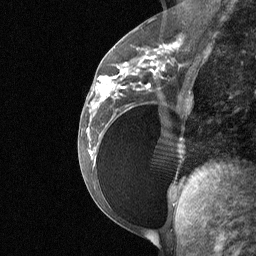
Breast MRI (dynamic contrast-enhanced), one sagittal slice; position 28 of 64 along the scan axis; dynamic contrast-enhanced study with each time point stored as its own series, time point 2 of 3 at this slice position (early post-contrast, ordered by acquisition time); 1.5 T; TE 4.8 ms, TR 27 ms; 256 × 256 image matrix, field of view 200 × 200 mm. Female patient, age 34 years. From the clinical record (not read from this slice): setting: breast cancer imaged before/during neoadjuvant chemotherapy; receptor status: HR-positive, HER2-negative.
Annotated regions visible in this slice (semi-automatically segmented with operator editing):
- analysis volume of interest (the breast-tissue region the enhancement analysis was run in; not a lesion): box from (x=92, y=50) to (x=188, y=185) px
- tumour enhancement mask (voxels above the 90 % enhancement threshold inside the analysis volume of interest): (x=93, y=56)–(x=155, y=108)